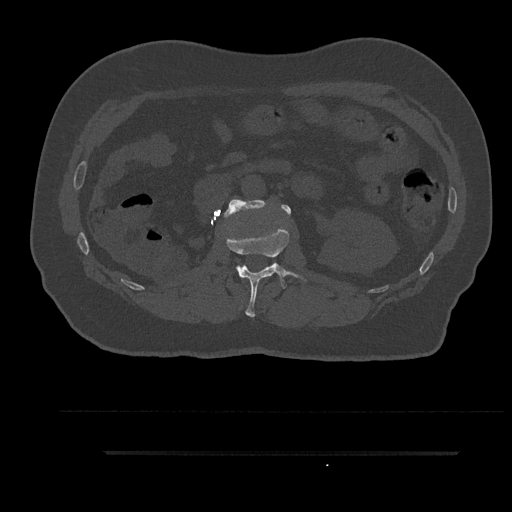
CT including the spine, one axial slice; position 159 of 797 along the scan axis; reconstruction kernel Br40s/3; 120 kVp; bone window (W 1800 / L 400 HU); 512 × 512 image matrix, field of view 432 × 432 mm. Male patient, age 63 years. From the clinical record (not read from this slice): primary cancer: renal; vertebrae with lytic lesions (as recorded): T8.
Structures marked on this image (semi-automatic segmentation, software-assisted and operator-edited):
- L1 vertebra: box from (x=226, y=227) to (x=302, y=317) px
- L2 vertebra: (x=224, y=199)–(x=291, y=218)